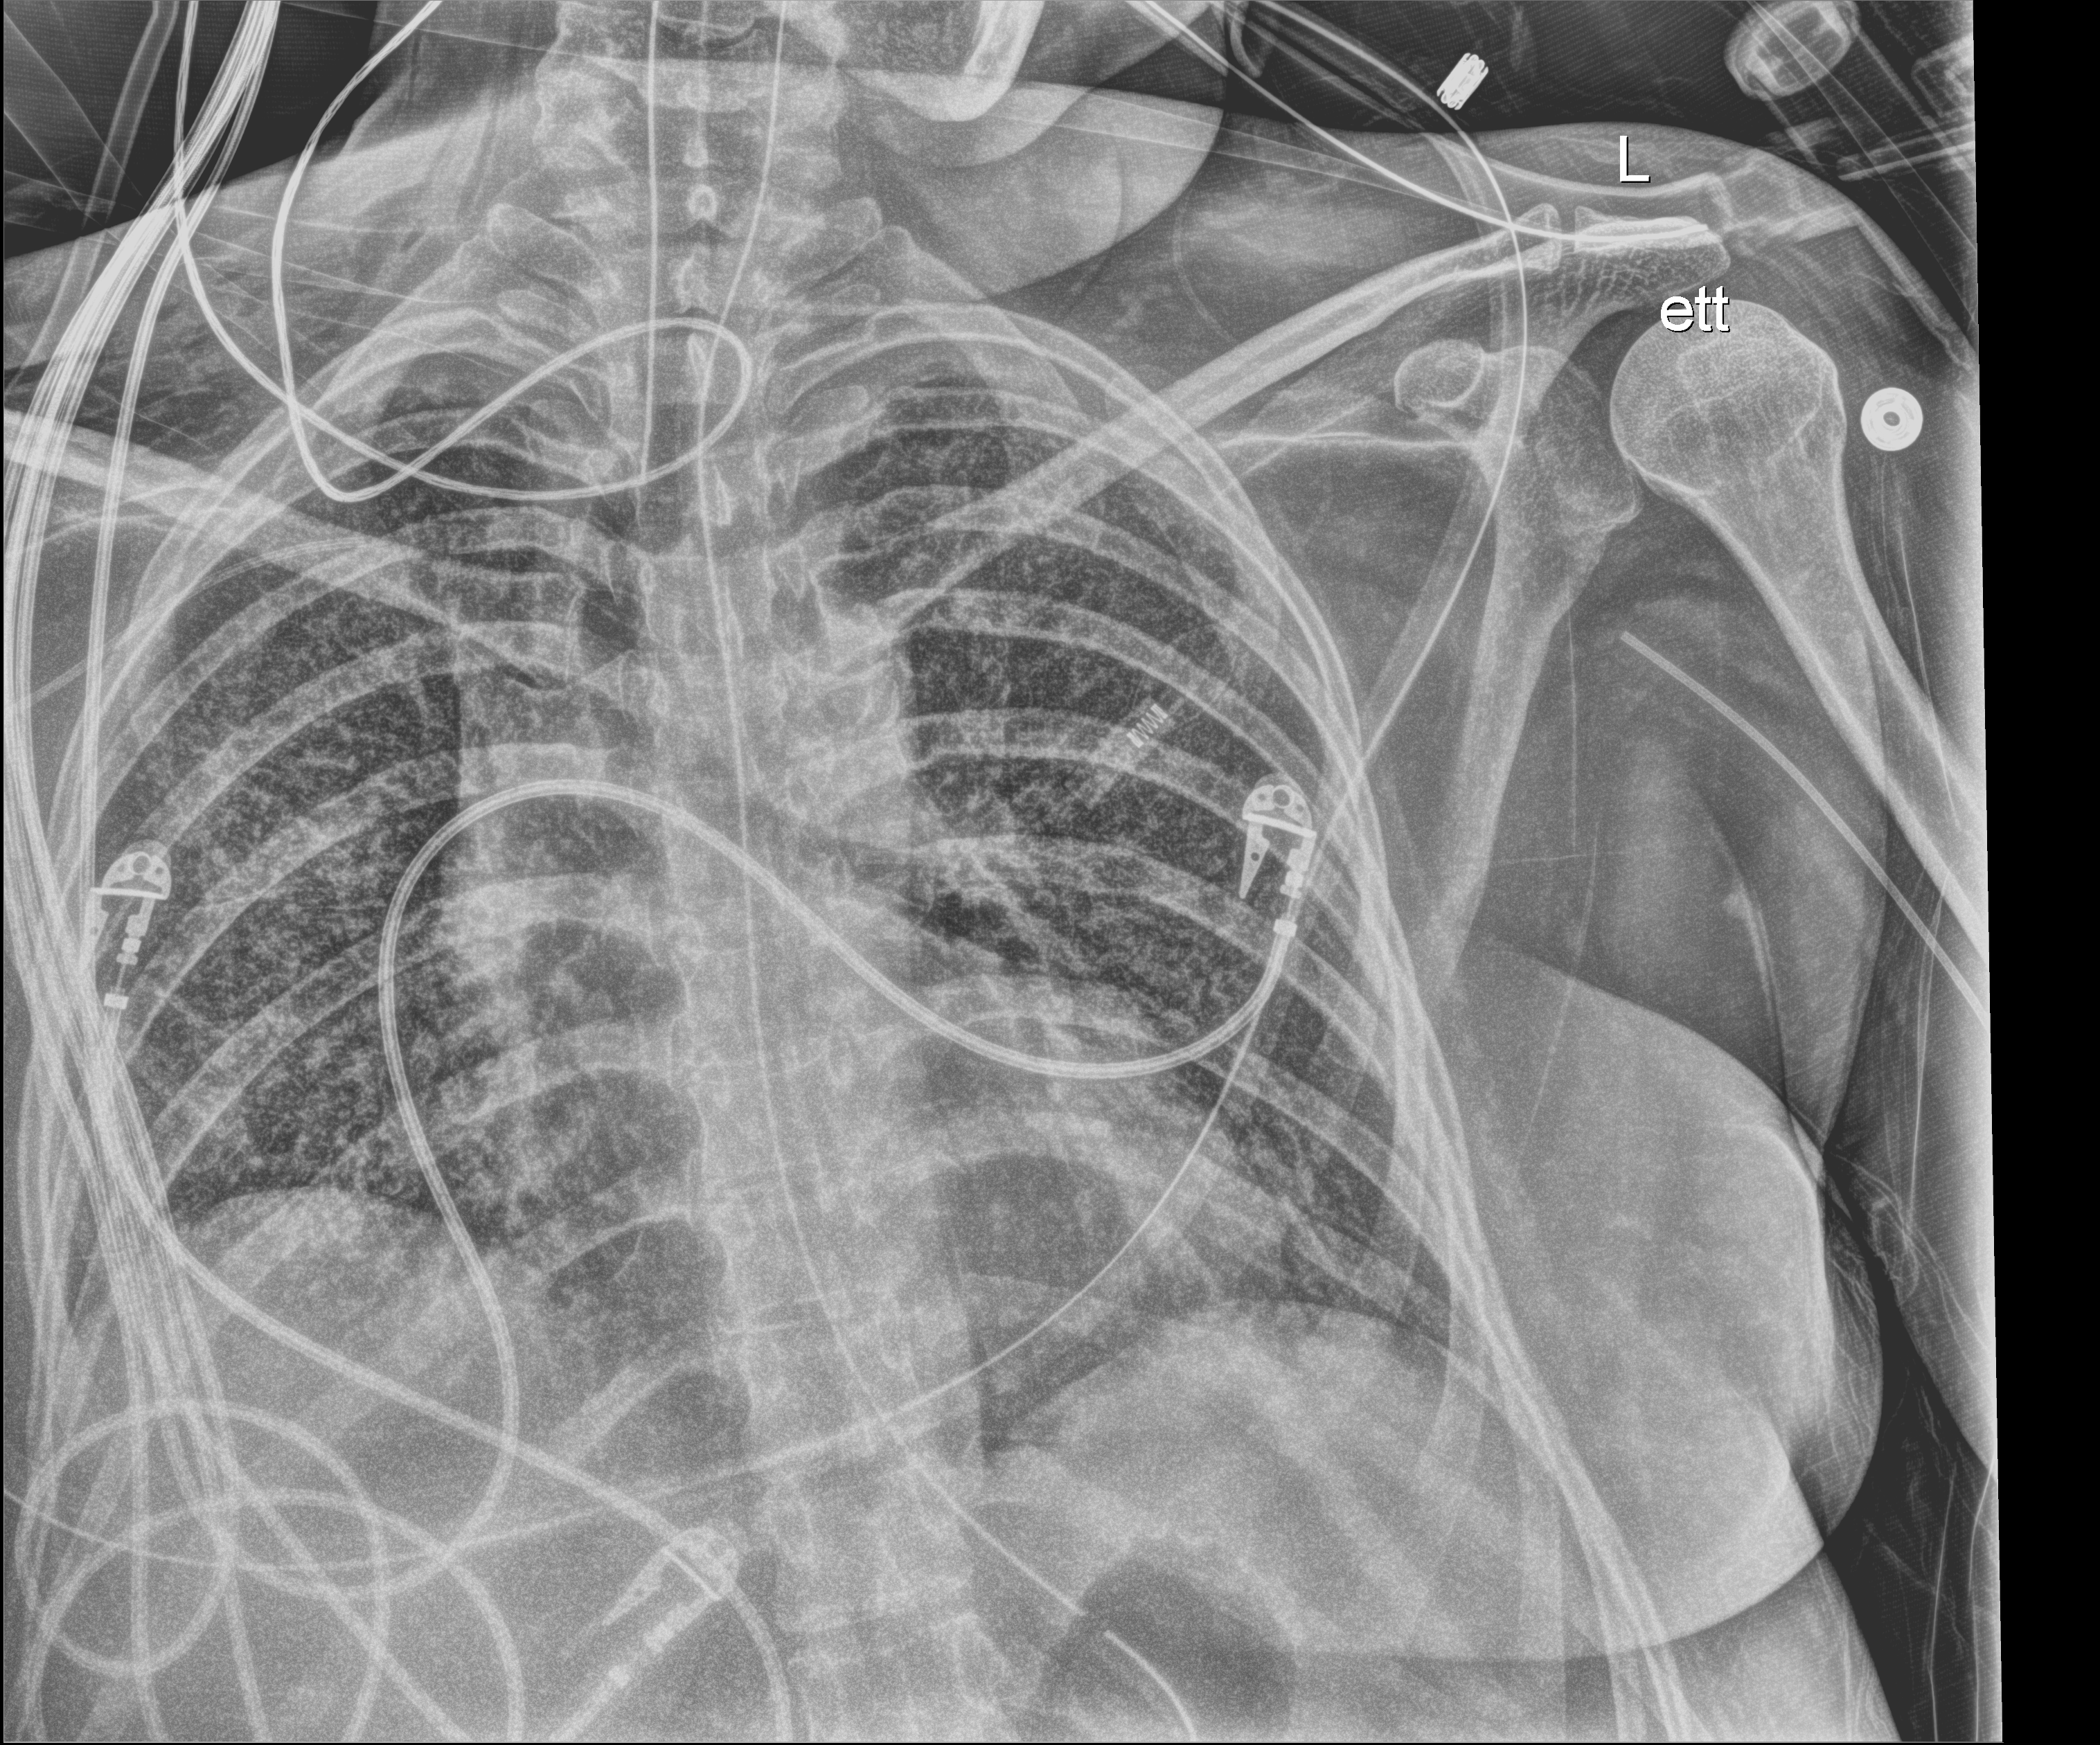
Chest radiograph (digital radiography). Patient hospitalised with COVID-19; female, aged 18–59 years.
From the hospital-stay record, not from the radiograph (when in the stay this image was taken is not recorded):
- length of hospital stay: 73 days
- hypertension (admission record): no